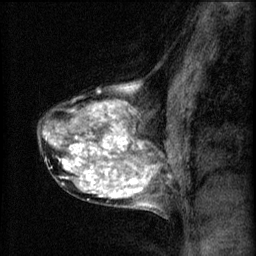
Breast MRI (dynamic contrast-enhanced), one sagittal slice. Slice 39 of 60 in the series (ordered by position). 3 images stored at this slice position (order not interpretable as contrast timing). 1.5 T. TE 4.2 ms, TR 8.2 ms. 2 mm slice thickness. 256 × 256 image matrix. Patient: female, 40 years.
Outlined on this slice (semi-automatic segmentation, software-assisted and operator-edited):
- analysis volume of interest (the breast-tissue region the enhancement analysis was run in; not a lesion): box from (x=37, y=80) to (x=167, y=211) px
- tumour enhancement mask (voxels above the 70 % enhancement threshold inside the analysis volume of interest): (x=44, y=84)–(x=159, y=207)